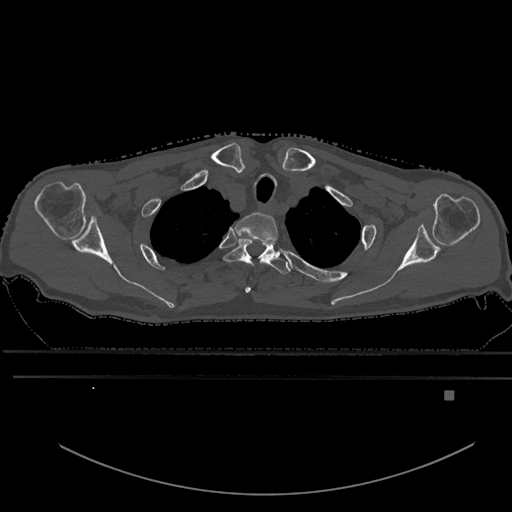
CT including the spine, one axial slice; slice 508 of 969 in the series (ordered by position); bone window (W 1800 / L 400 HU); 0.5 mm slice thickness; 512 × 512 image matrix, field of view 456 × 456 mm. Male patient, age 82 years. Case-level facts recorded for this patient, not image findings: primary cancer: prostate; vertebrae with lytic lesions (as recorded): T11, T9, T8, T2.
Annotated regions visible in this slice (semi-automatically segmented with operator editing):
- T1 vertebra: bounding box [x1, y1, x2, y2] px = [235, 212, 279, 293]
- T2 vertebra: [223, 239, 291, 275]